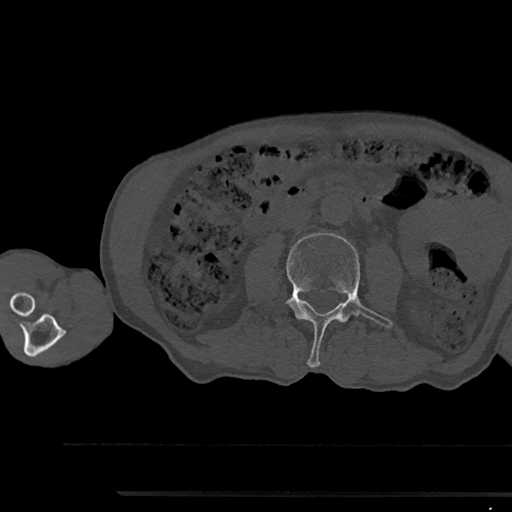
CT including the spine, one axial slice; slice 488 of 797 in the series (ordered by position); reconstruction kernel Br40s/3; 120 kVp; bone window (W 1800 / L 400 HU); 512 × 512 image matrix. Patient: male, 79 years. From the clinical record (not read from this slice): primary cancer: prostate.
Structures marked on this image (semi-automatic segmentation, software-assisted and operator-edited):
- L3 vertebra: bounding box [x1, y1, x2, y2] px = [286, 233, 392, 367]